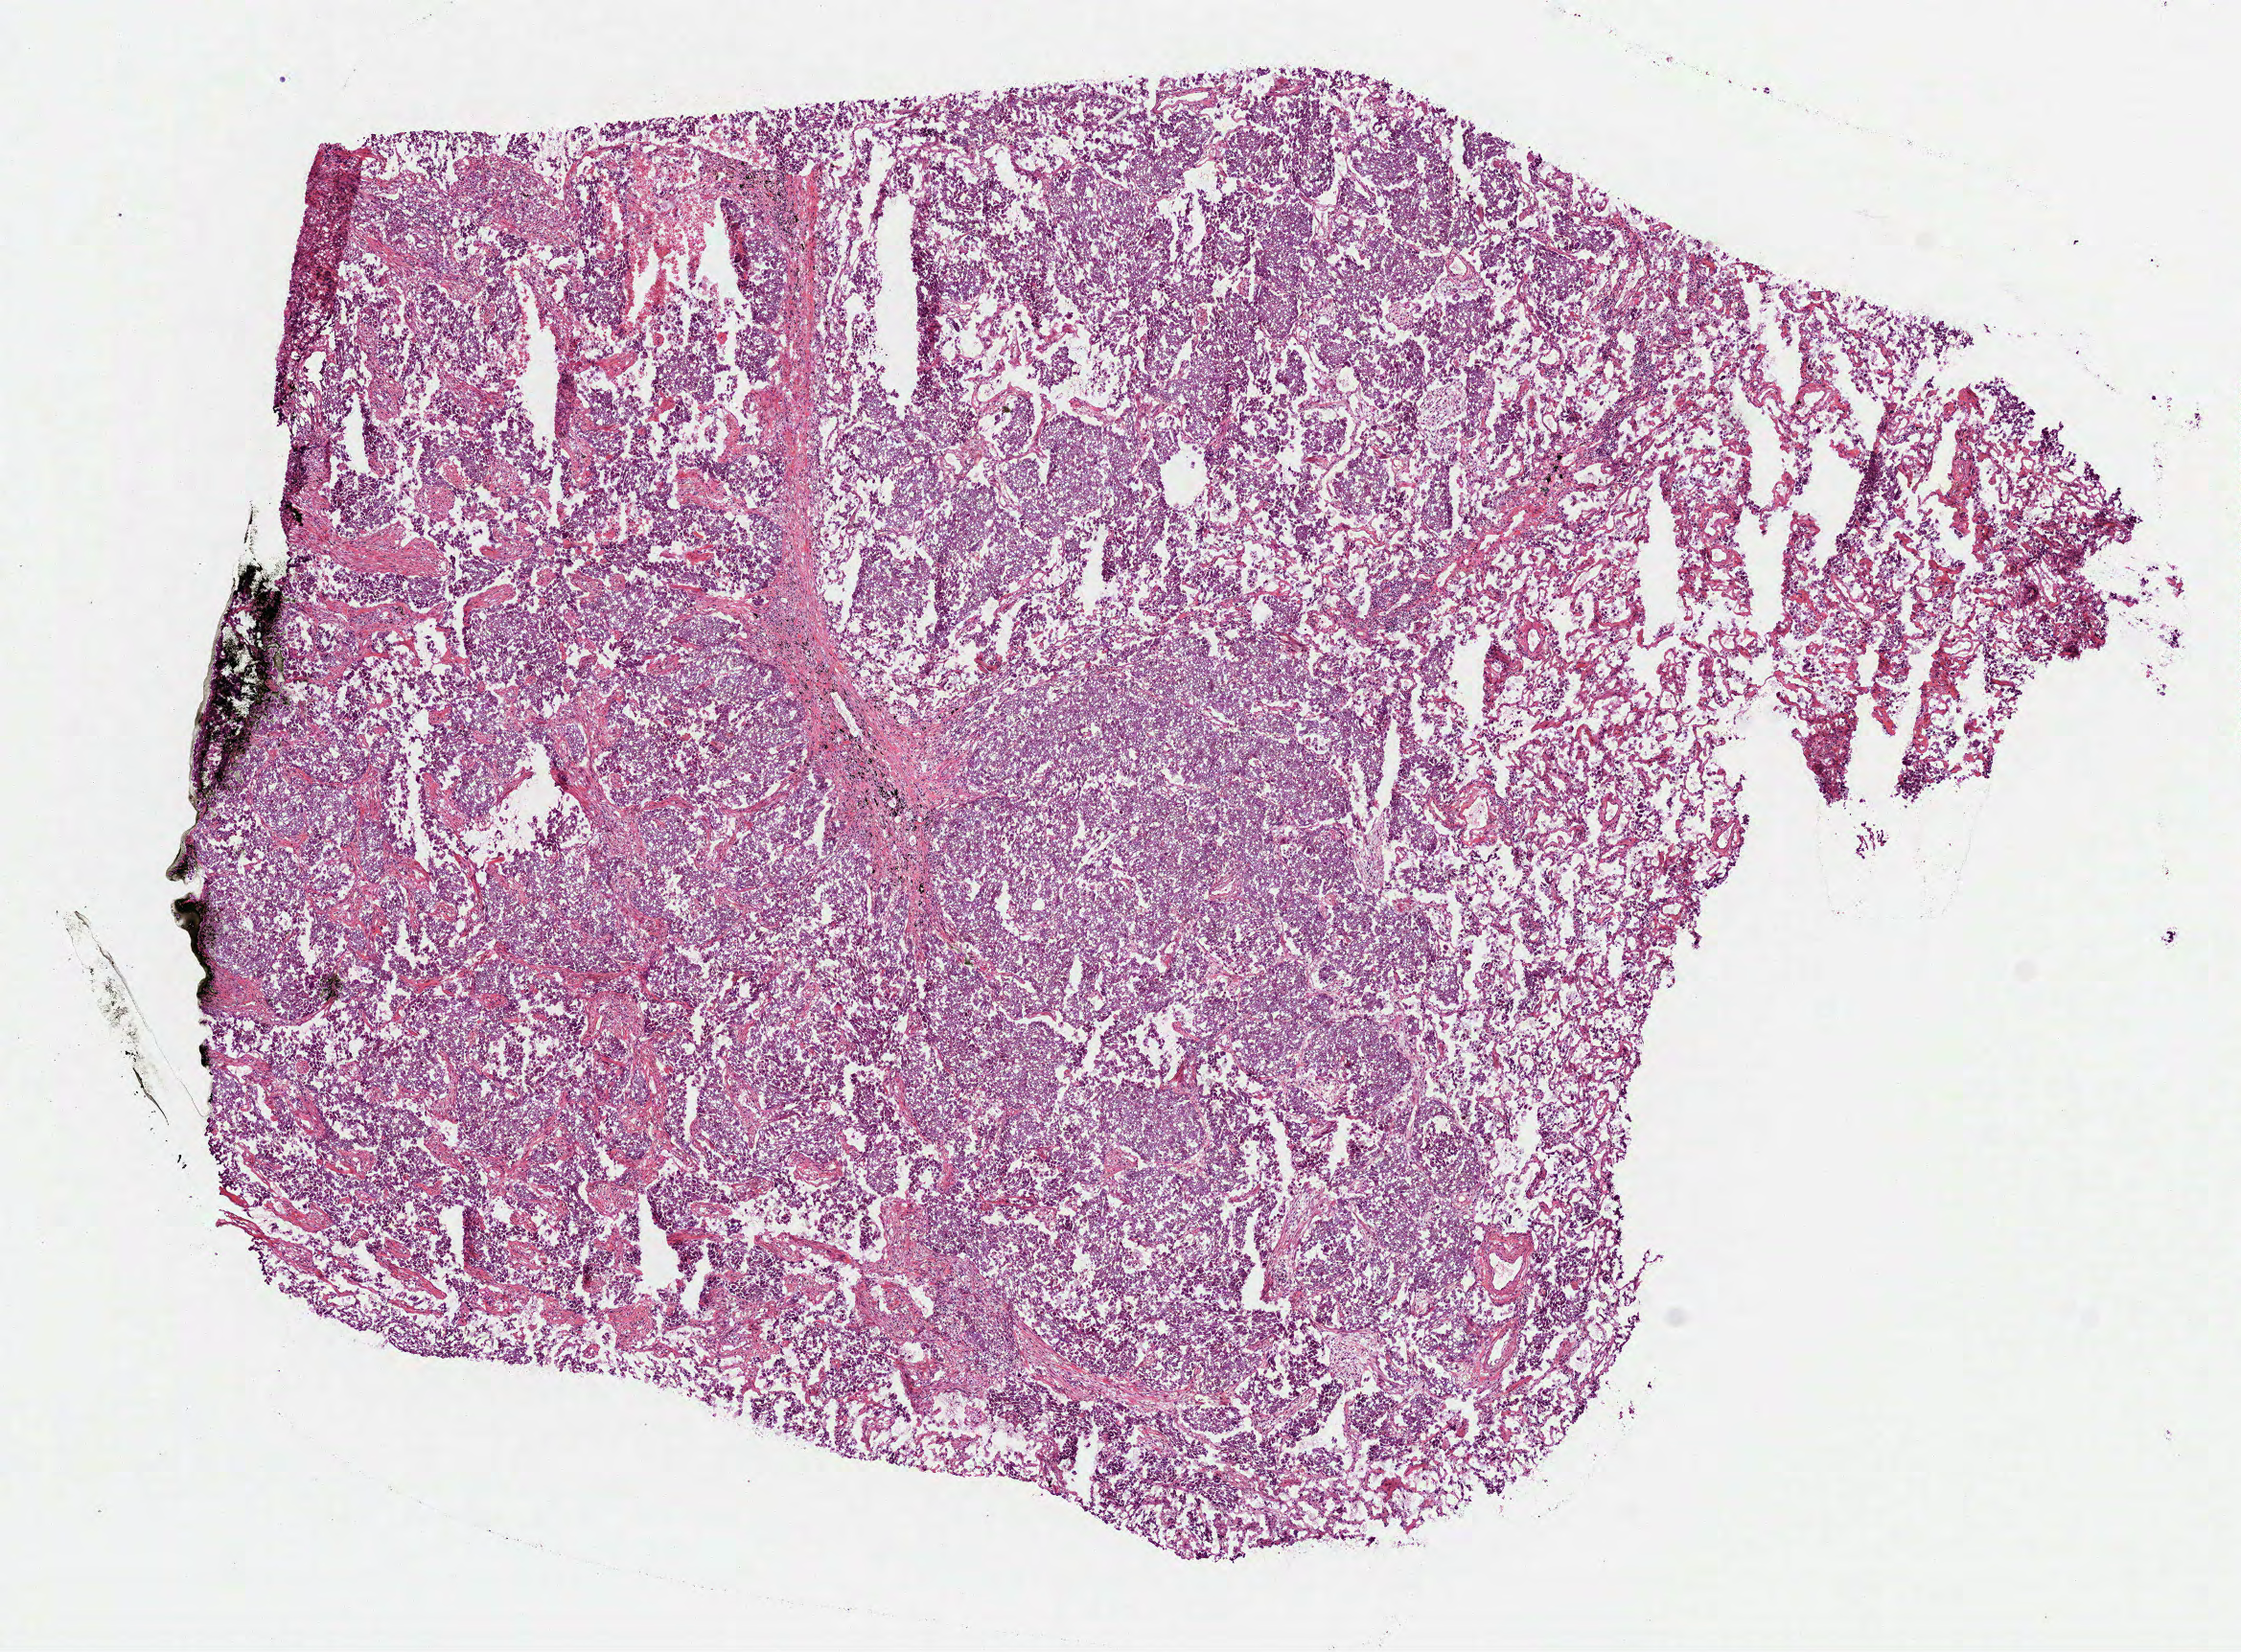
H&E-stained whole-slide image, shown as a low-resolution overview of the whole scanned area (about 9.4 x 7.0 mm, acquisition: 40x scan). Frozen section from the bottom of the tissue portion. Lung, primary tumour sample. Patient: male, age at initial diagnosis 72 years. Composition of this section per pathologist review: tumour cells 75%, tumour nuclei 75%, normal cells 12%, stromal cells 10%, necrosis 3%.
• pathologic diagnosis: Adenocarcinoma, NOS (upper lobe, lung)
• AJCC pathologic stage: IIIA (6th edition)
• TNM: T3 N2 M0